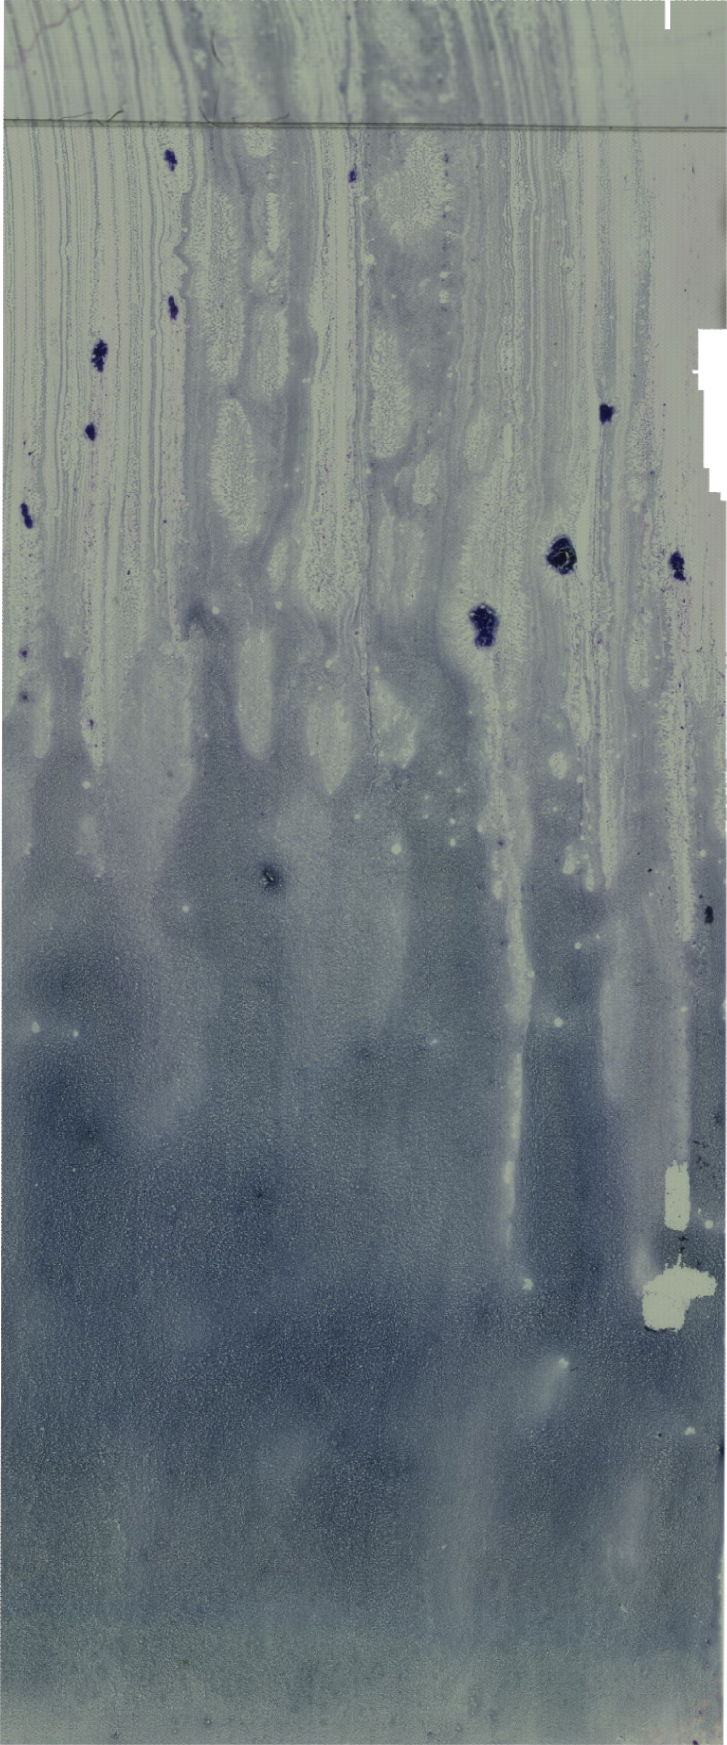
Bone marrow aspirate smear, May-Grünwald–Giemsa stain, whole-slide image — whole scanned area (about 20.6 x 49.5 mm) shown as a low-resolution overview. Patient sex: male.
Diagnosis: T Acute Lymphoblastic Leukemia.